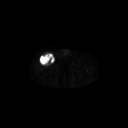
FDG PET of an extremity soft-tissue mass (from a PET/CT study), one axial slice. Slice 296 of 311 in the series (ordered by position). 3.27 mm slice thickness. 128 × 128 image matrix, field of view 700 × 700 mm. Male patient, age 56 years. Case-level facts recorded for this patient, not image findings: histological type: pleiomorphic leiomyosarcoma; grade: intermediate; site of the primary tumour: right thigh.
Outlined on this slice (expert contour drawn on MRI and transferred to this co-registered scan by the dataset authors):
- gross tumour volume including surrounding oedema: bounding box (x1, y1, x2, y2) in pixels: (39, 52, 55, 66)
- gross tumour volume (mass): (40, 52, 55, 66)